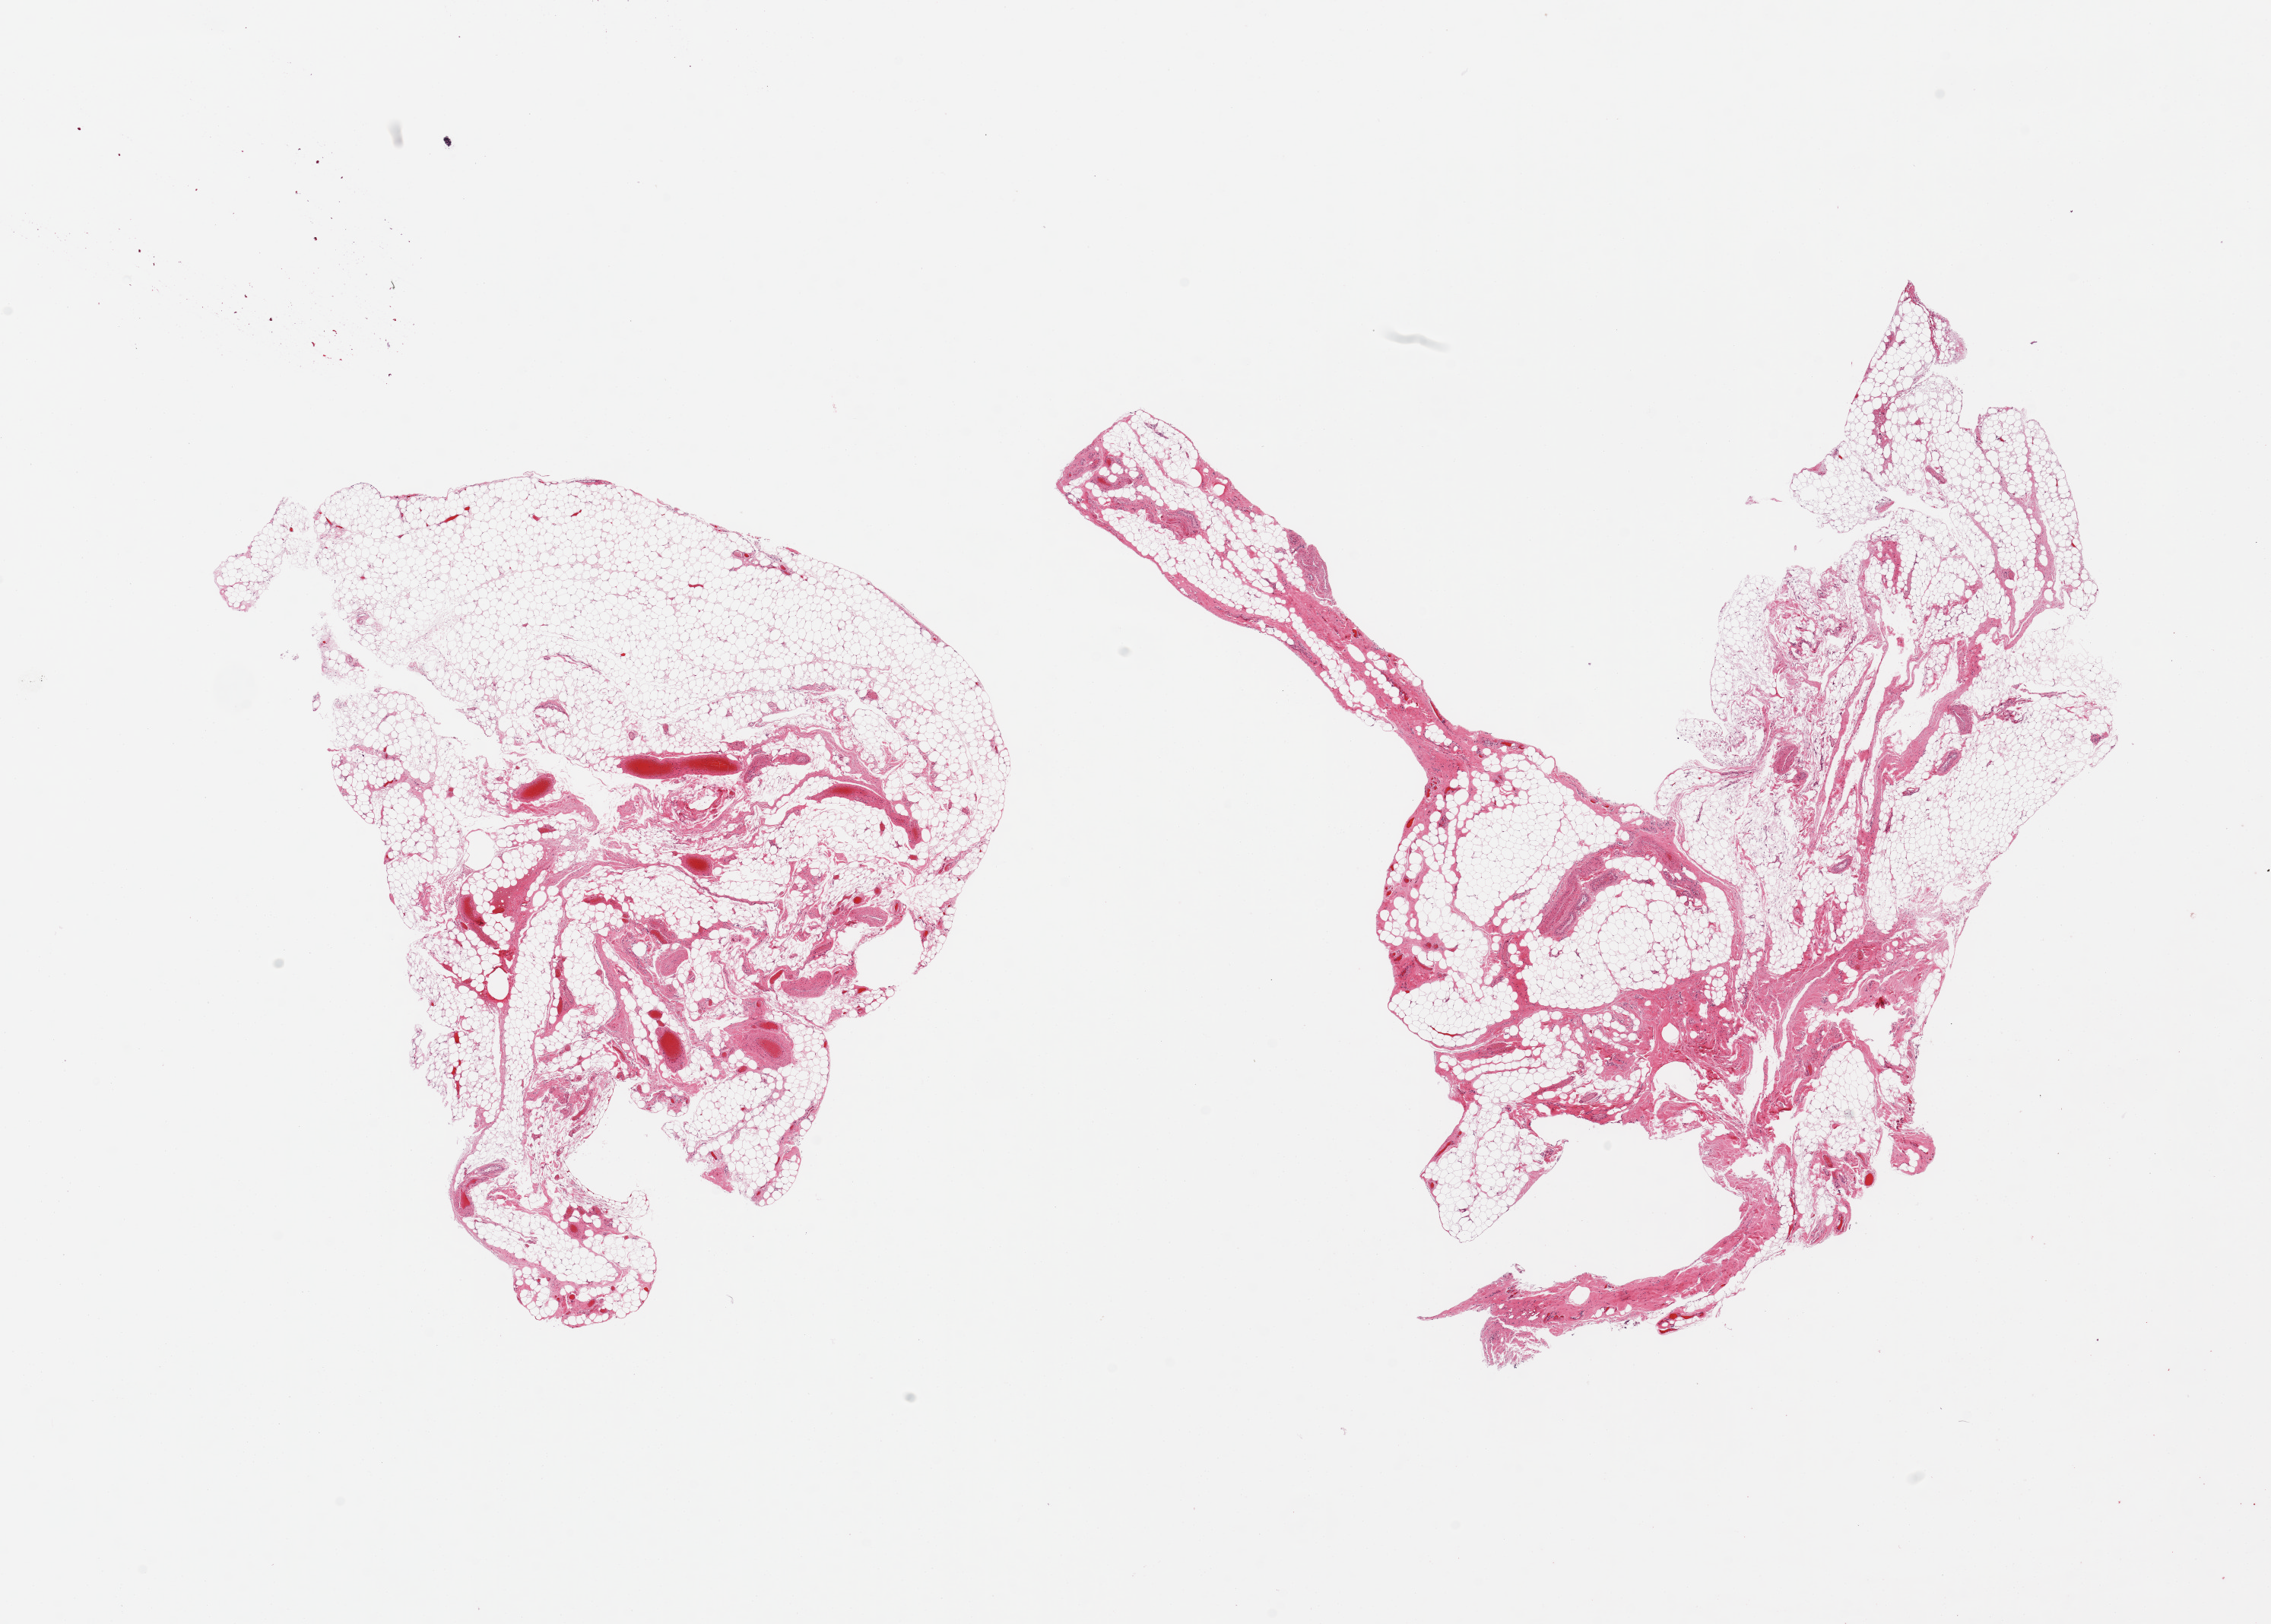
Haematoxylin and eosin whole-slide image, brightfield — low-resolution overview of the scanned area, about 23.6 x 16.9 mm (from a 20x scan); PAXgene-fixed paraffin-embedded (PFPE) section; target tissue: omentum; tissue donor sample. Male donor.
Reviewer comment on this tissue sample: 2 pieces ~30% fascia/vascular elements.